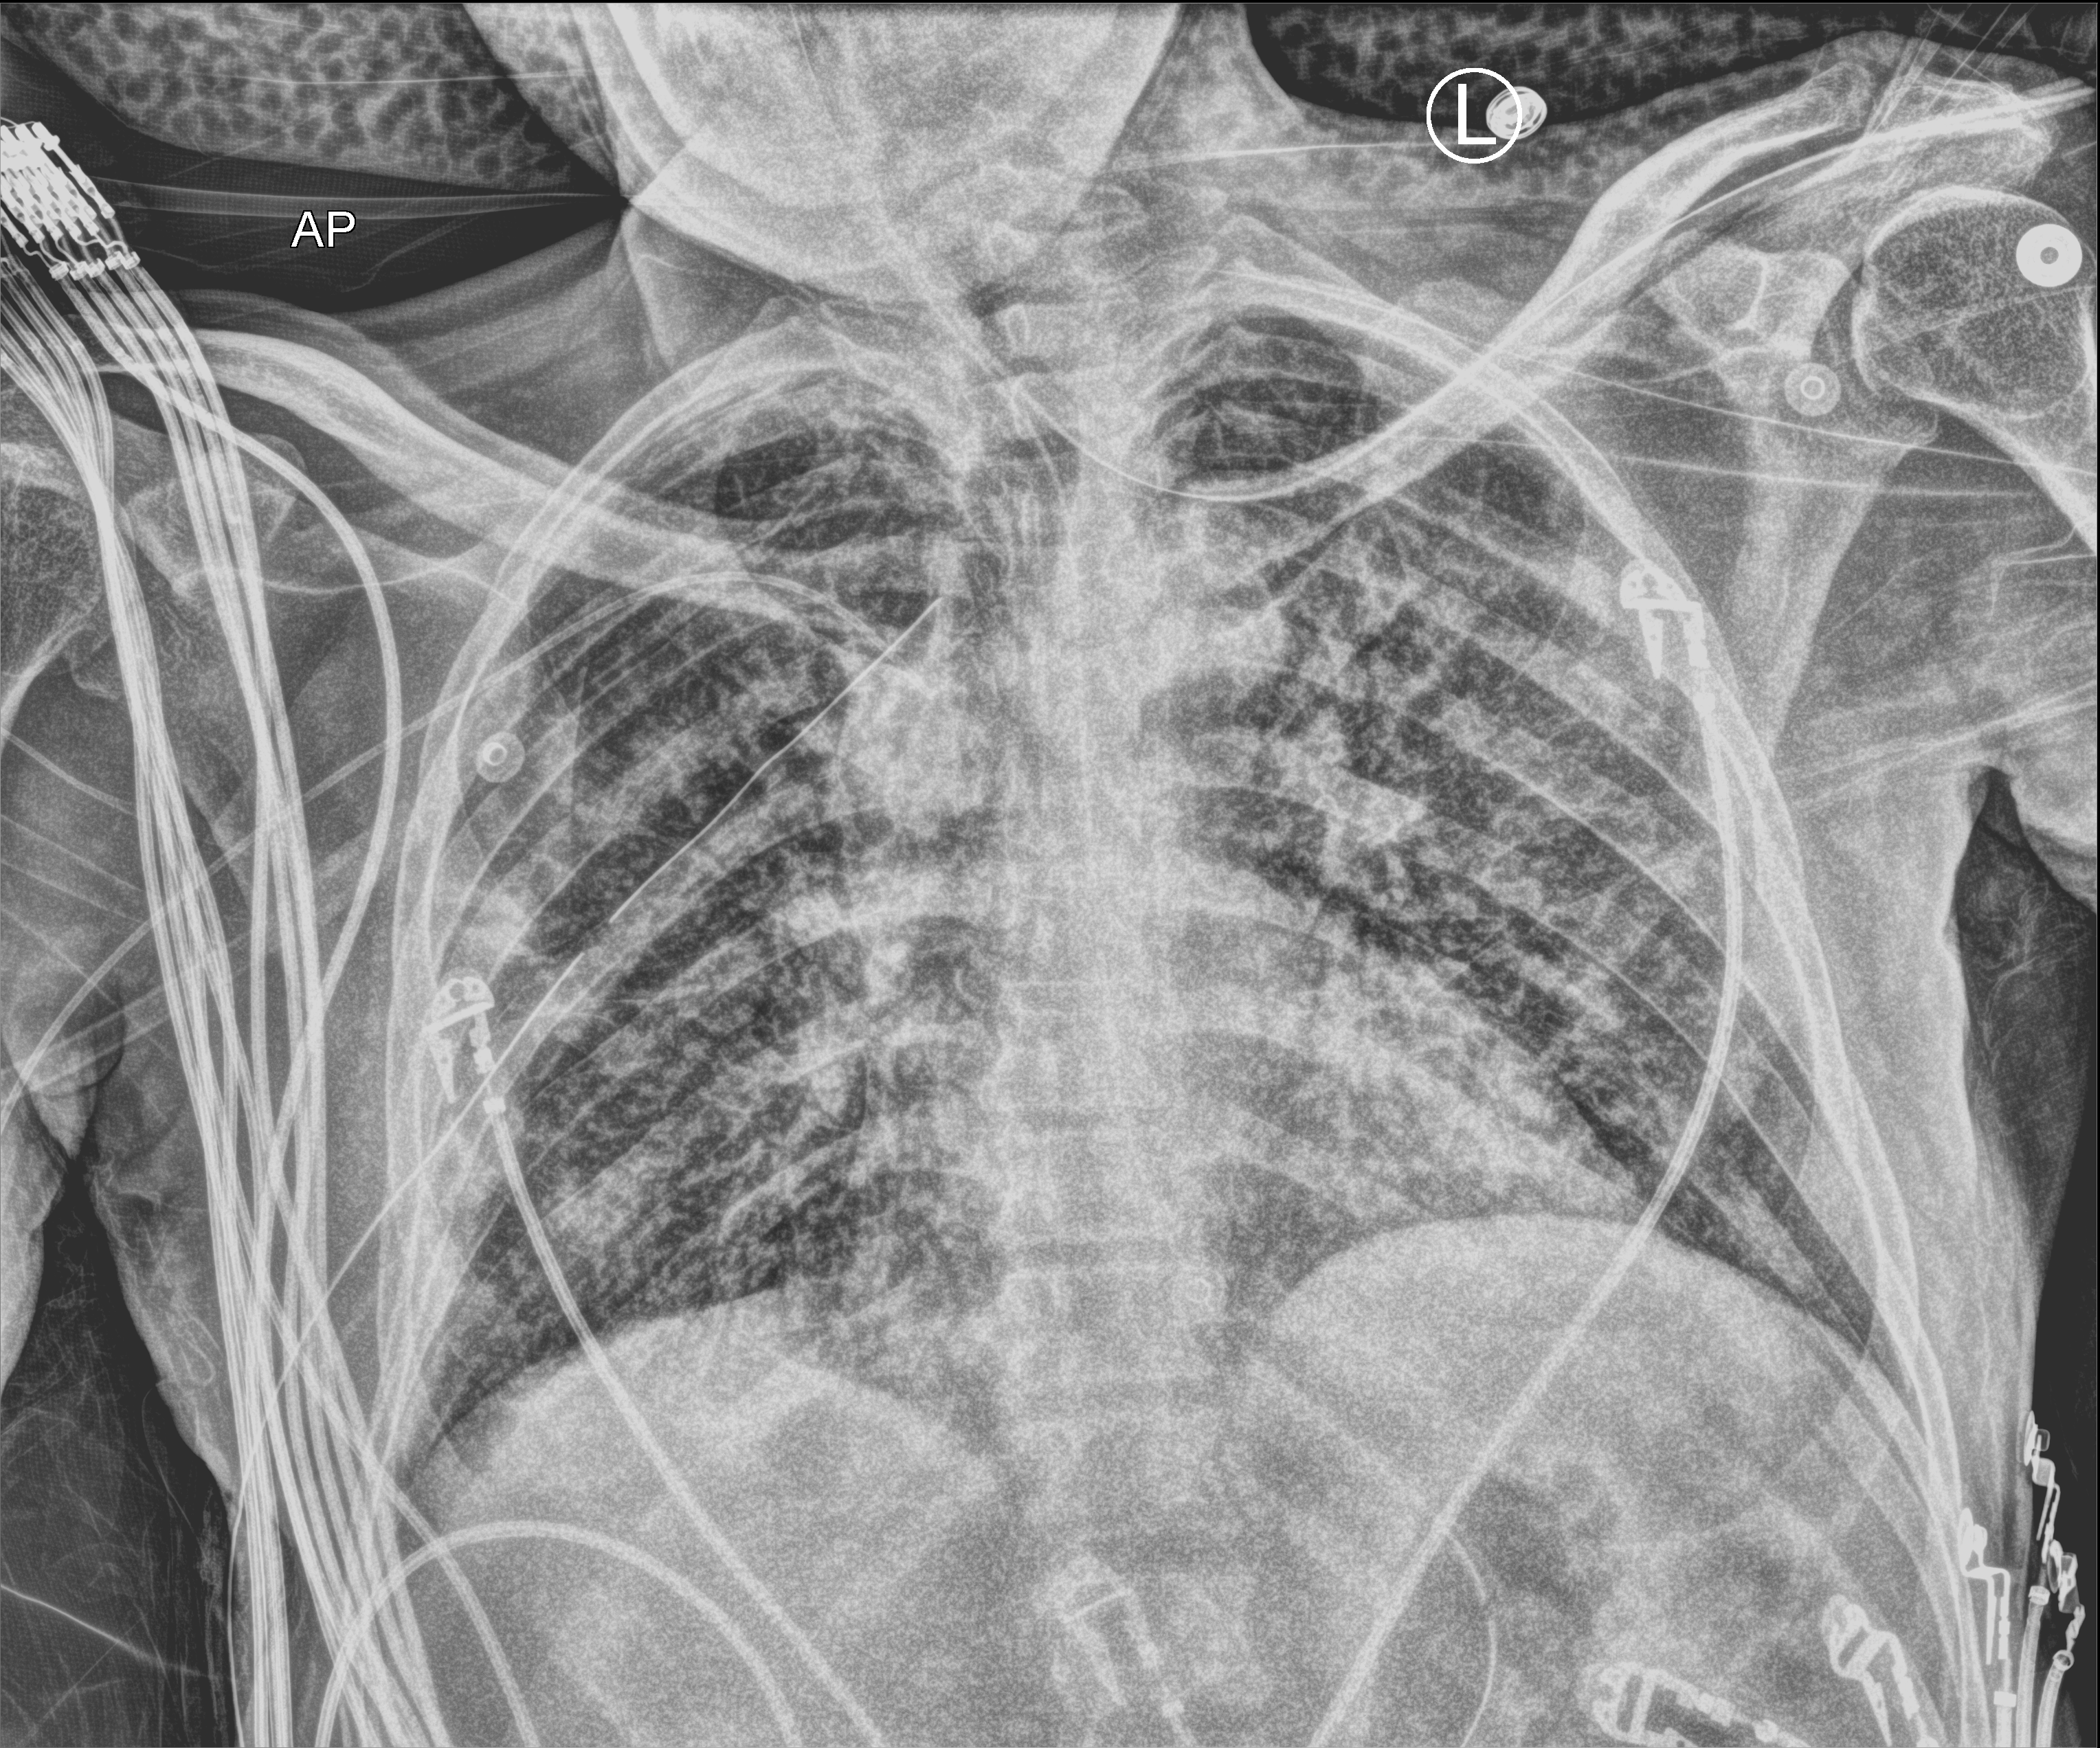
Chest X-ray (portable). Male patient hospitalised with COVID-19, age 18–59 years.
Admission-level facts for this patient (not findings on this image; timing relative to this image not recorded): COPD (admission record): no; admitted to intensive care during this hospital stay: yes; diabetes (admission record): yes.